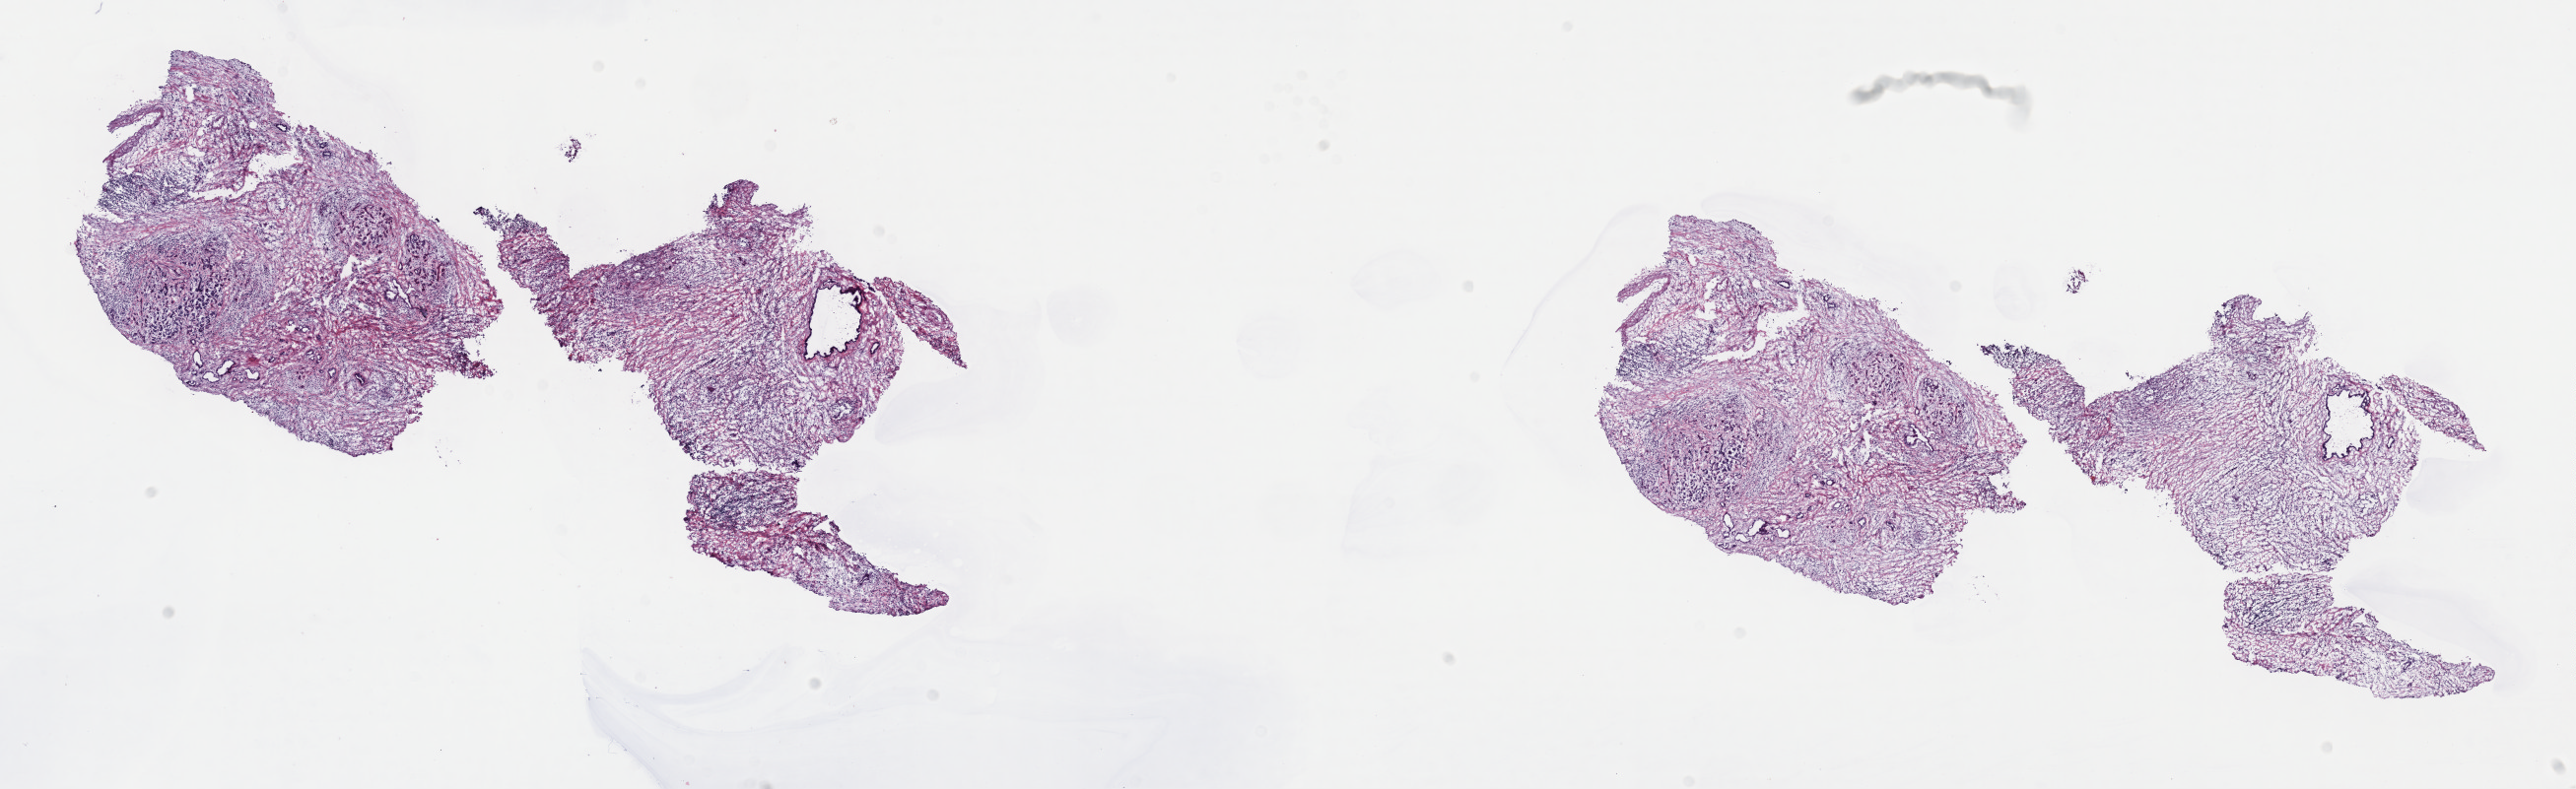
Hematoxylin and eosin (H&E) stained whole-slide image, whole scanned area (about 21.1 x 6.5 mm, from a 40x scan) shown as a low-resolution overview. Frozen section from the top of the tissue portion. Sample: primary tumour, pancreas. Female patient; age at initial diagnosis 60 years. Histologic grade: G2 (moderately differentiated). Composition of this section per pathologist review: tumour cells 60%, tumour nuclei 60%, normal cells 0%, stromal cells 40%, necrosis 0%. Inflammatory infiltration, as recorded: lymphocyte infiltration 70%, monocyte infiltration 10%, neutrophil infiltration 10%.
• TNM: T2 N0 M0
• lymph nodes positive (case pathology): 0 of 20 examined
• histologic diagnosis: Infiltrating duct carcinoma, NOS (head of pancreas)
• AJCC pathologic stage: IB (7th edition)